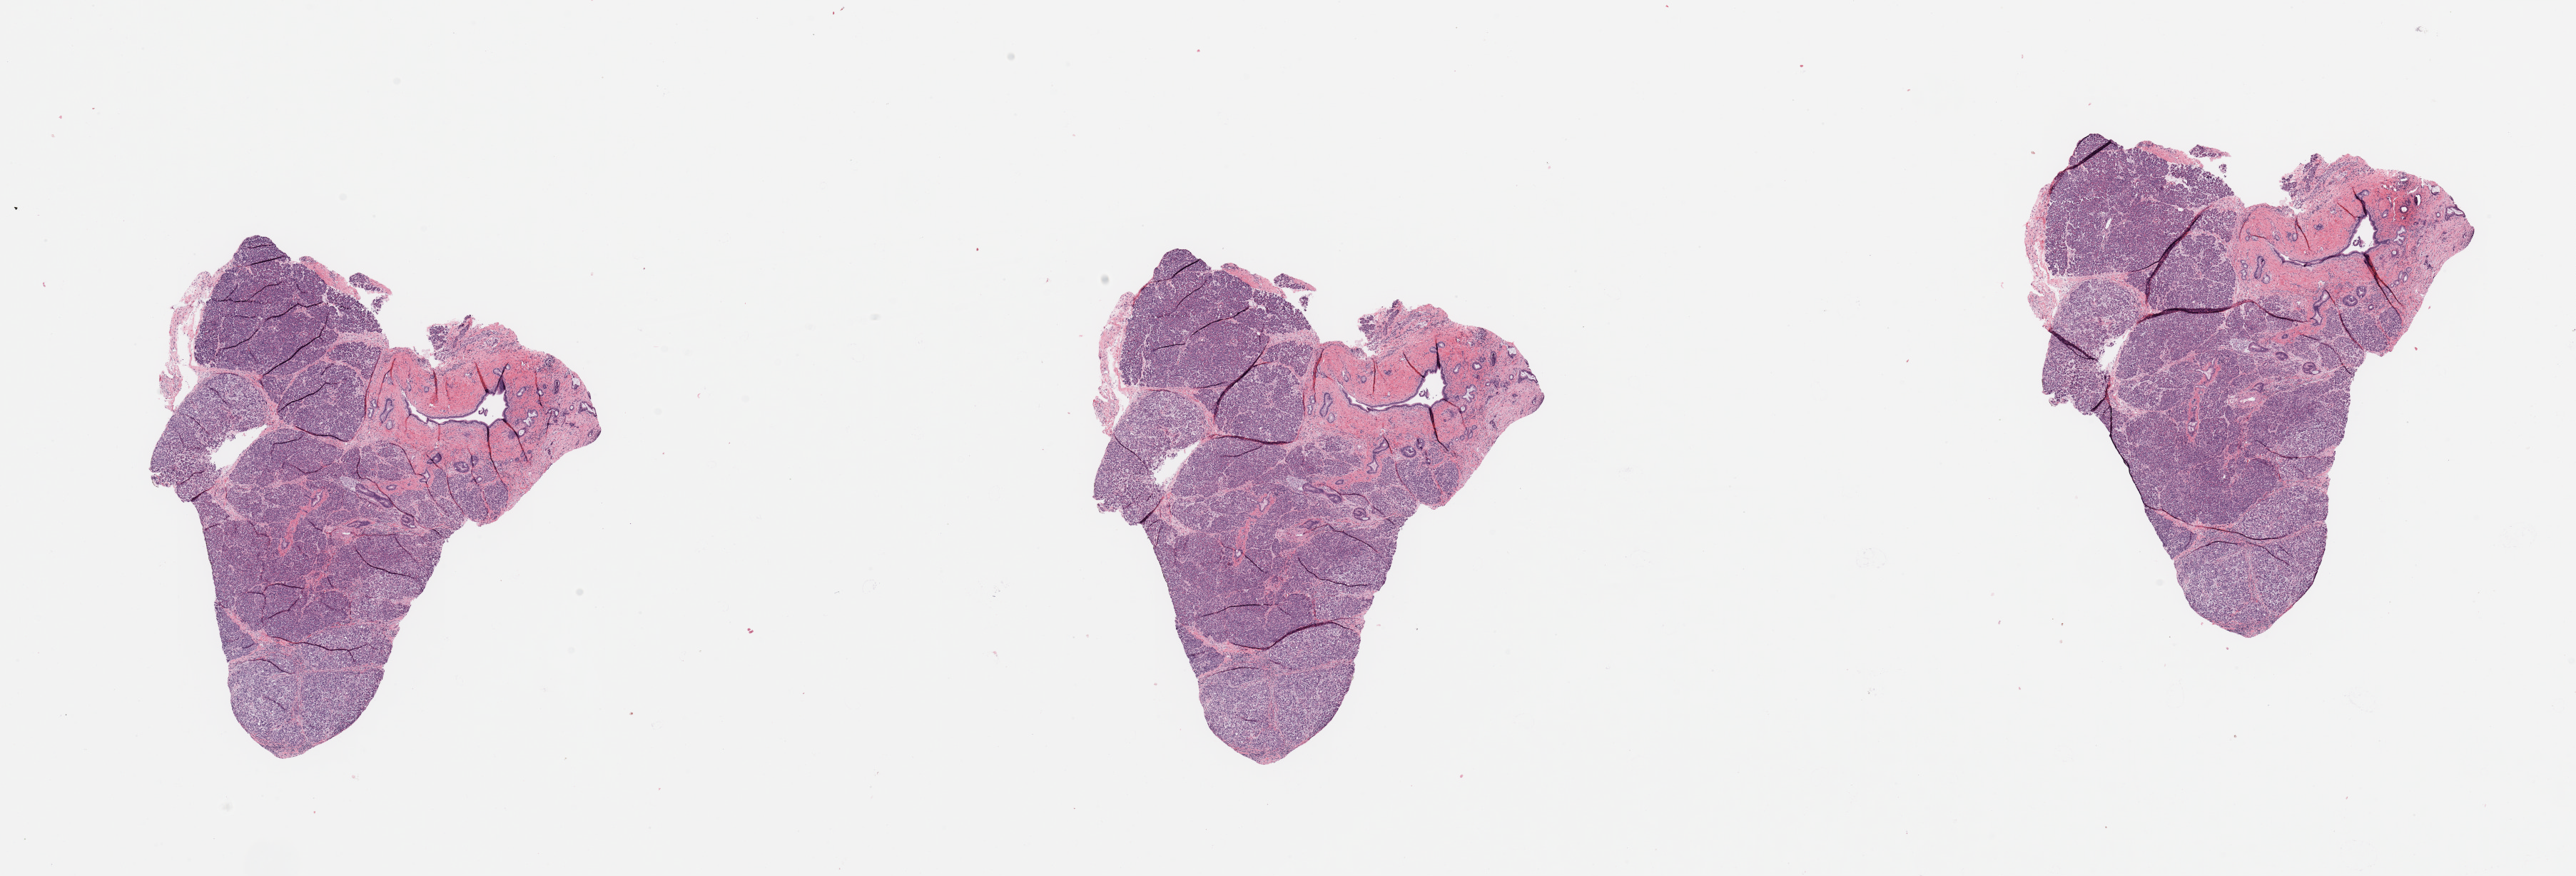
Digitized Hematoxylin and eosin (H&E) stained tissue section (whole slide) — a low-resolution overview of the entire scanned area, about 28.5 x 9.7 mm, normal (non-tumour) tissue sample, sampled site: pancreas. Female, 34 y/o.
This section: normal (non-tumour) tissue from the same patient. Patient diagnosis: Infiltrating duct carcinoma, NOS.